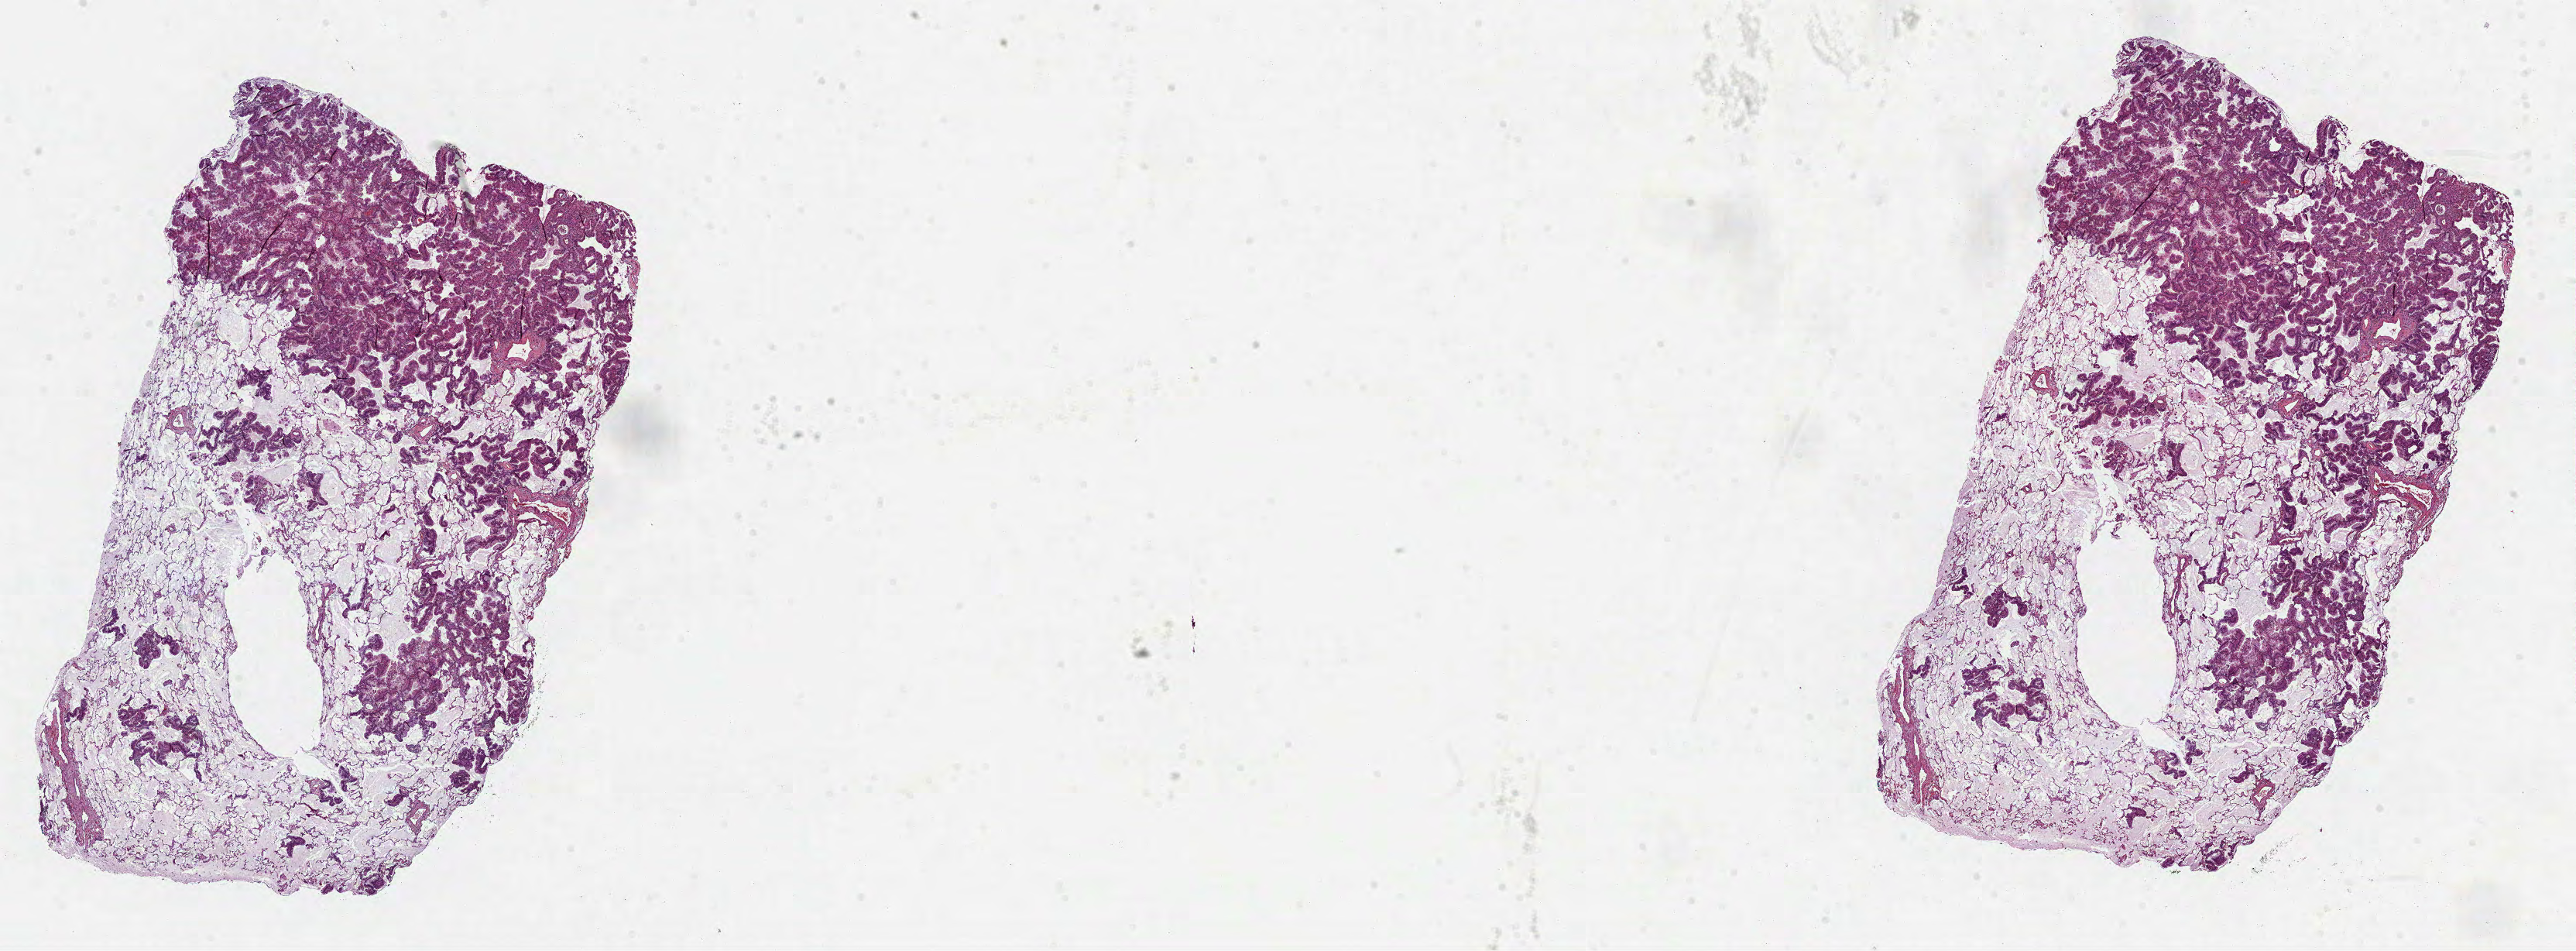
H&E-stained whole-slide image, a low-resolution overview of the entire scanned area, about 26.8 x 9.9 mm (from a 40x scan). FFPE section. Primary tumour sample from the lung. Male, age 64 years at initial diagnosis.
Diagnosis: Mucinous adenocarcinoma (lower lobe, lung). AJCC pathologic stage: IIB (7th edition). TNM: T3 N0 M0.